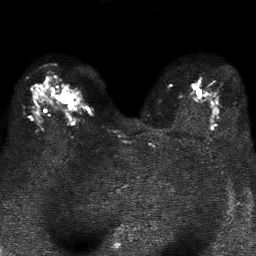
Breast MRI, one axial slice; position 24 of 37 along the scan axis; diffusion-weighted series; image 2 of 4 stored at this slice position (different b-values; order by instance number); 1.5 T; 5 mm slice thickness; 256 × 256 image matrix, field of view 320 × 320 mm. Female patient.
Annotated regions visible in this slice (outlined manually by an expert reader):
- tumour on diffusion-weighted imaging: bounding box (x1, y1, x2, y2) in pixels: (58, 92, 69, 101)